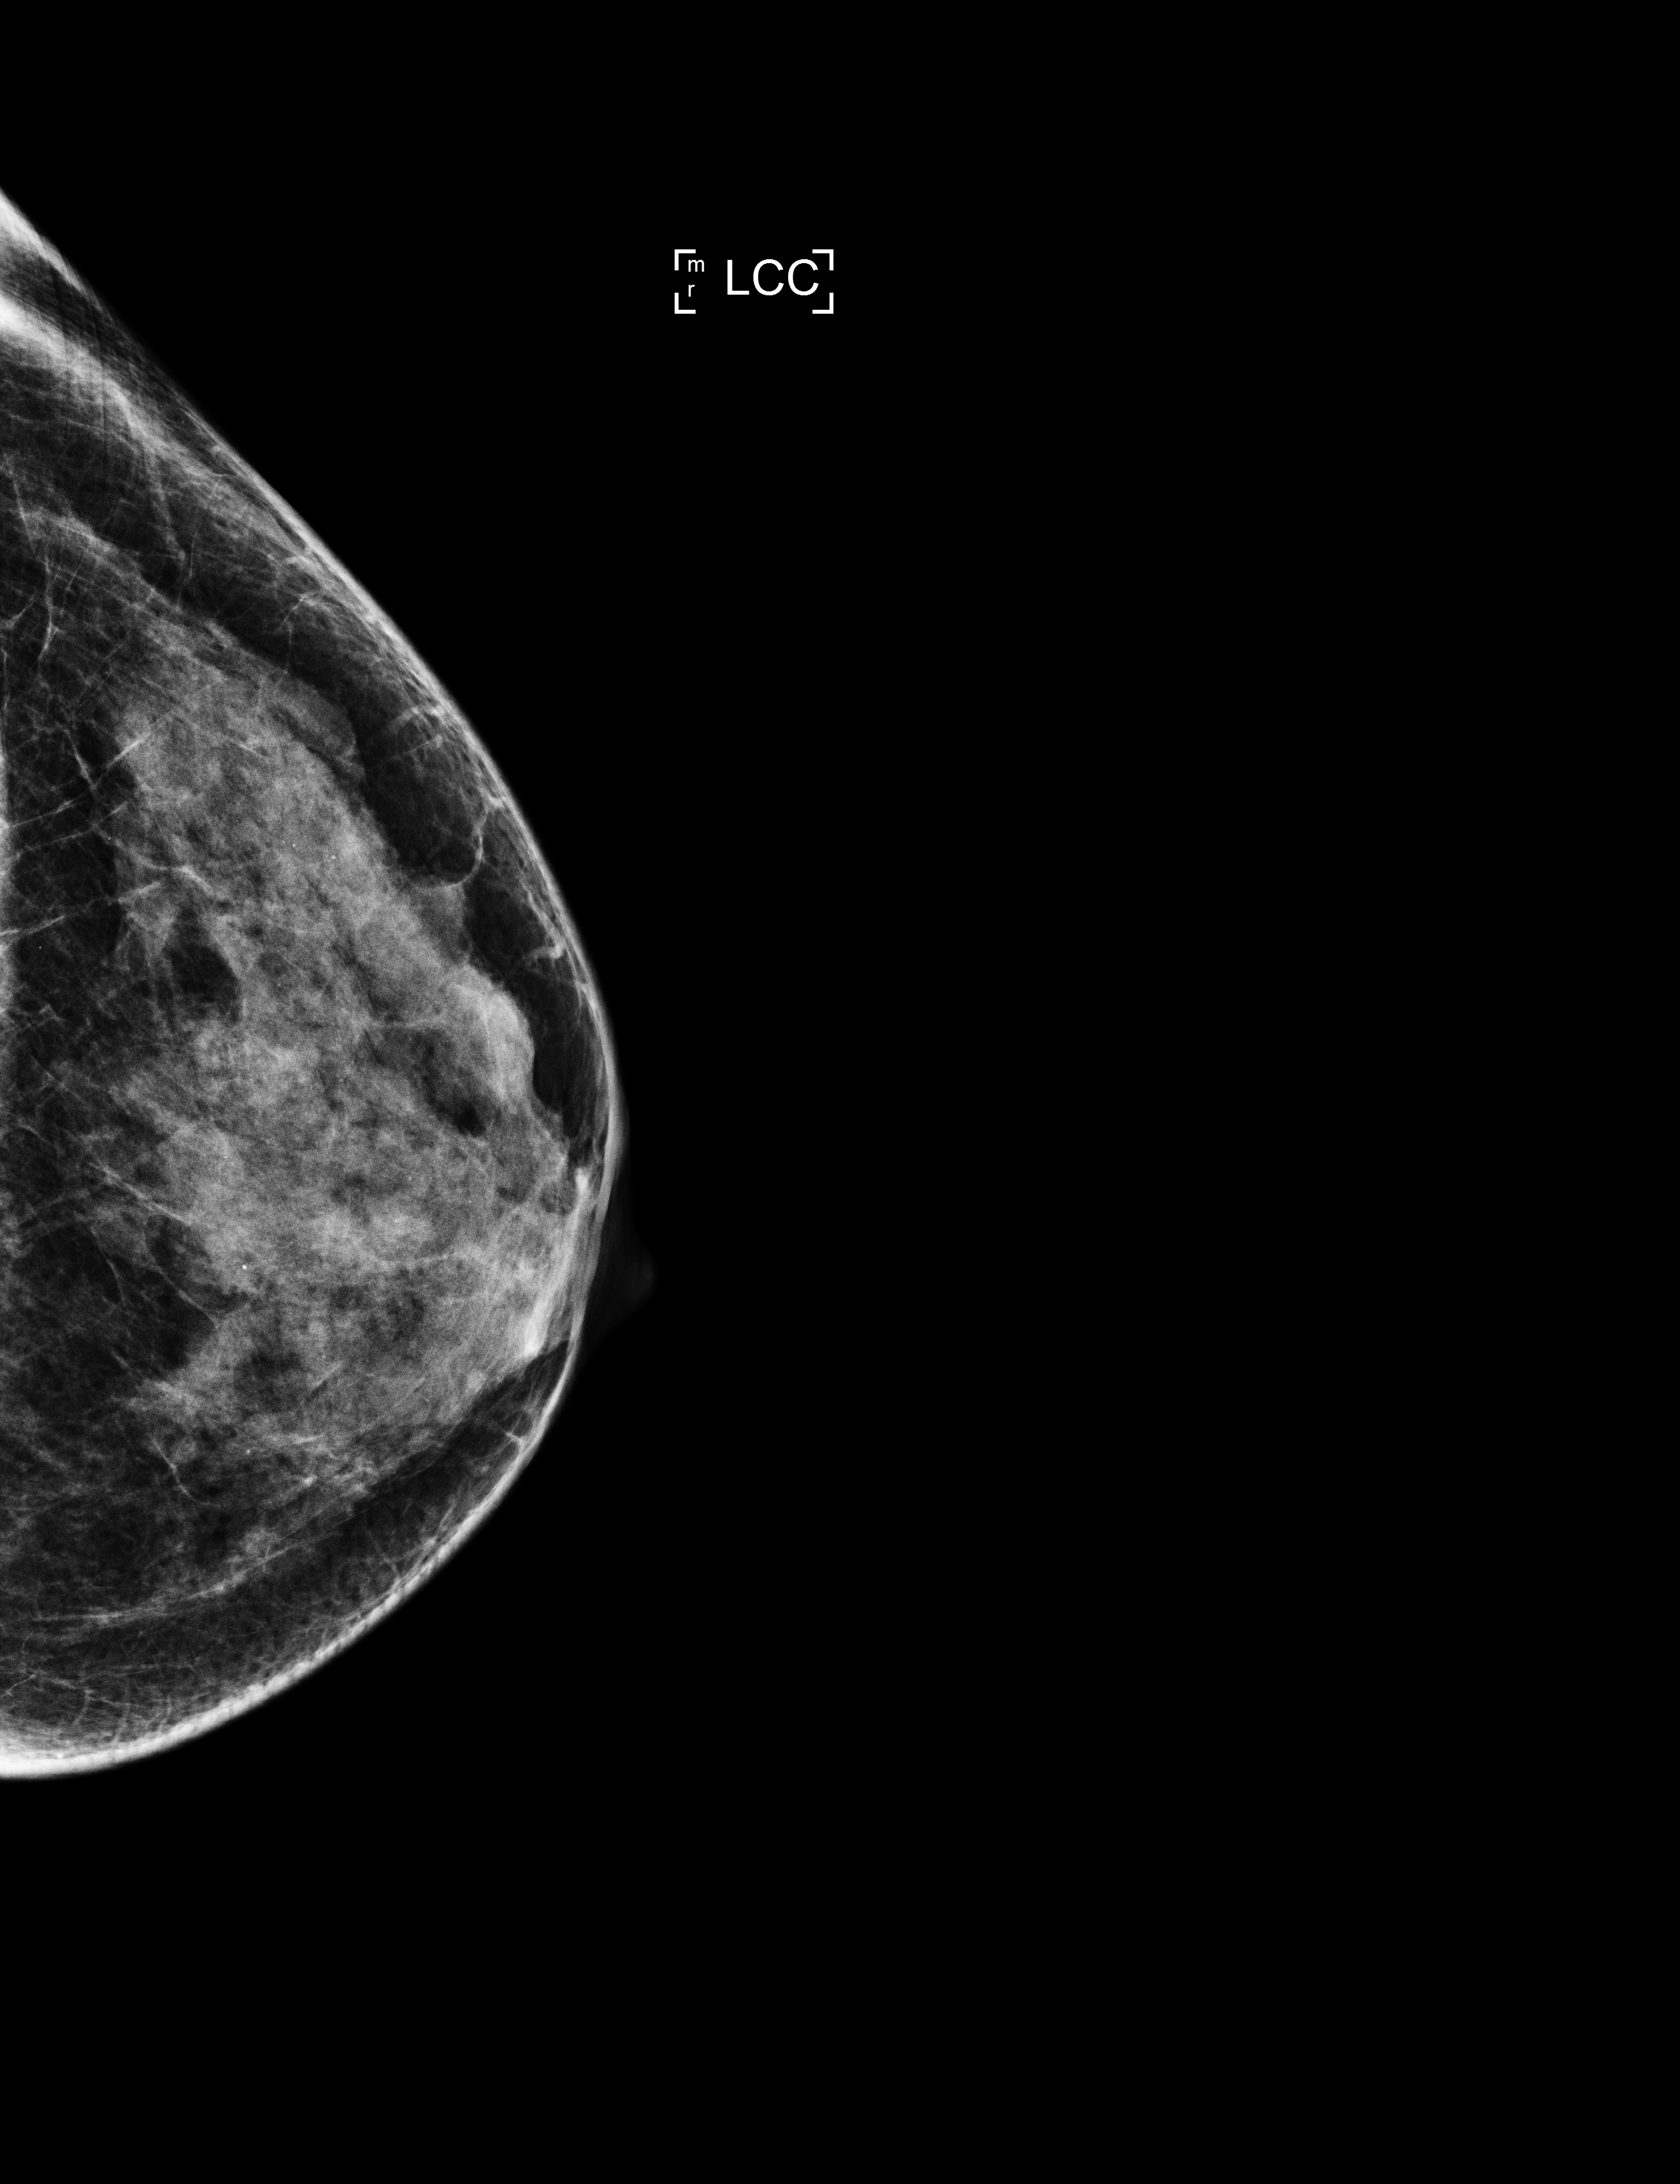
Digital mammogram (FFDM), left breast, cranio-caudal projection, annual screening mammography examination, compressed breast thickness 38 mm, system: Selenia Dimensions. Patient aged 50 years (female).
- breast density at the screening exam (both breasts): extremely dense (BI-RADS density category d)
- final BI-RADS category for the screening round (tomosynthesis exam, both breasts): category 3
- recall: recalled for additional imaging after this screen